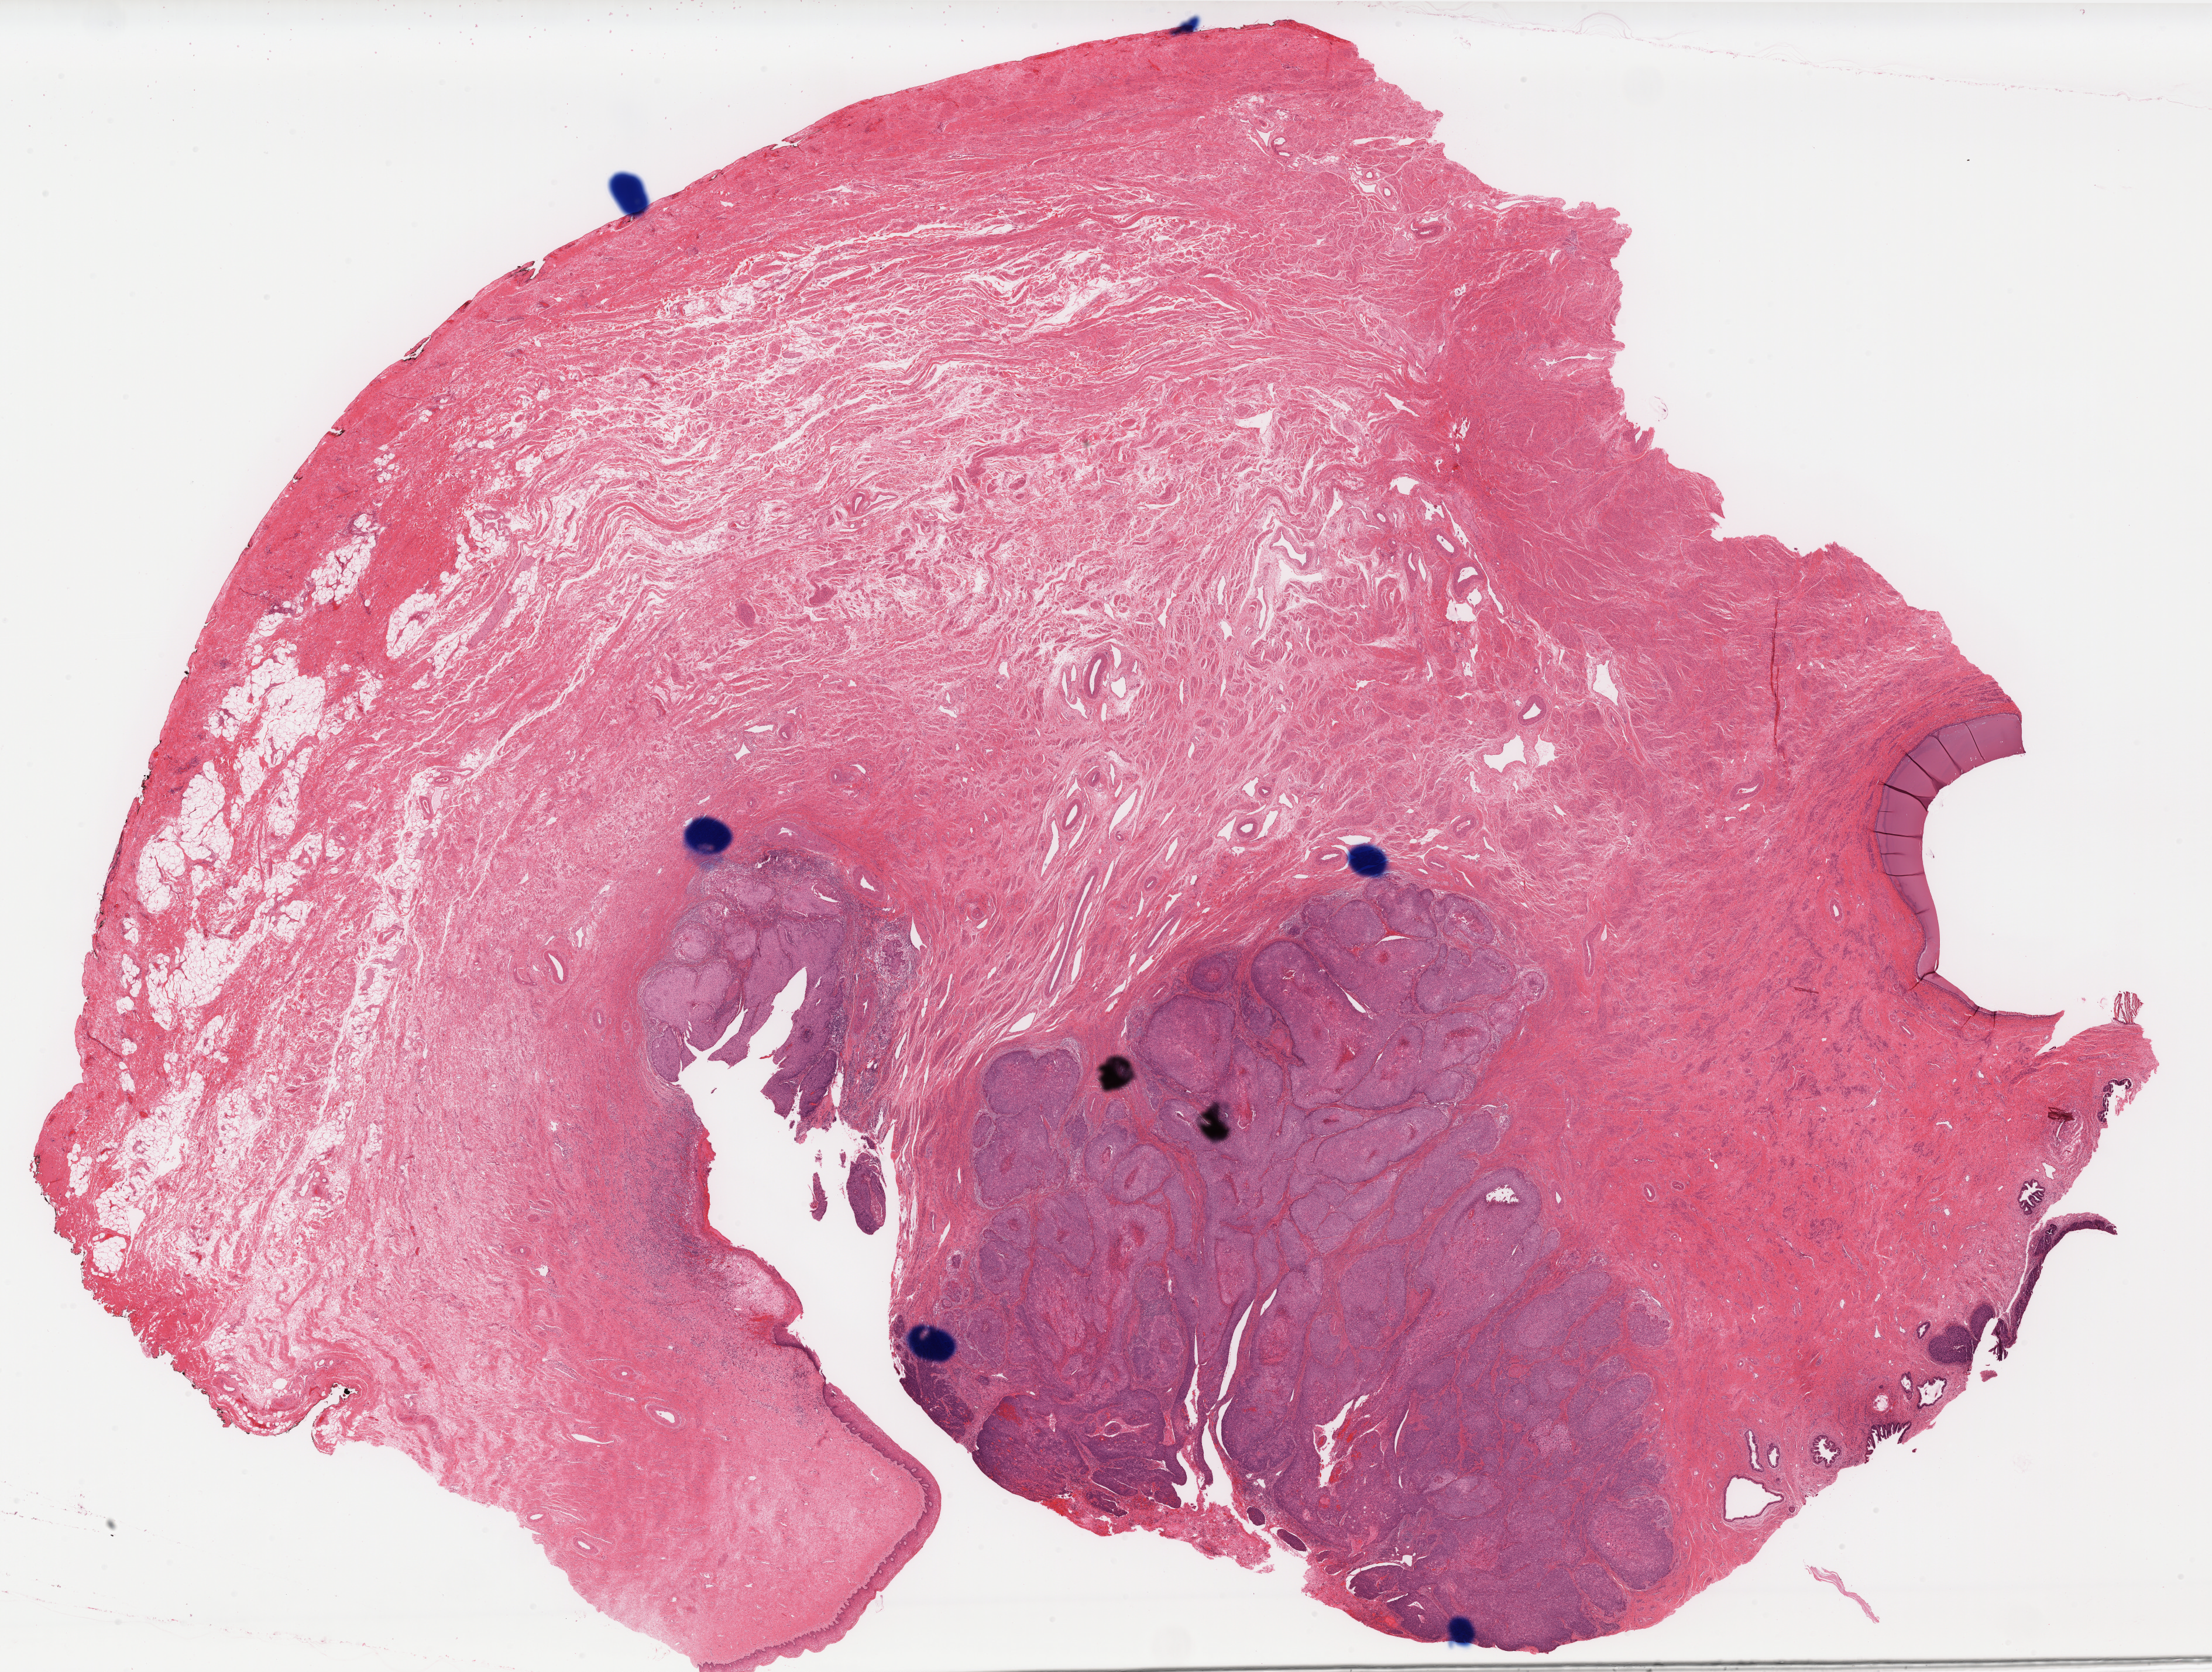
H&E-stained whole-slide image — whole scanned area (about 30.3 x 22.9 mm) shown as a low-resolution overview, formalin-fixed paraffin-embedded (FFPE) diagnostic section, cervix, primary tumour sample. Female, age 43 years at initial diagnosis. Histologic grade: G2 (moderately differentiated).
• histologic diagnosis: Squamous cell carcinoma, NOS (cervix uteri)
• FIGO stage: IB1
• lymph nodes positive (case pathology): 0 of 13 examined